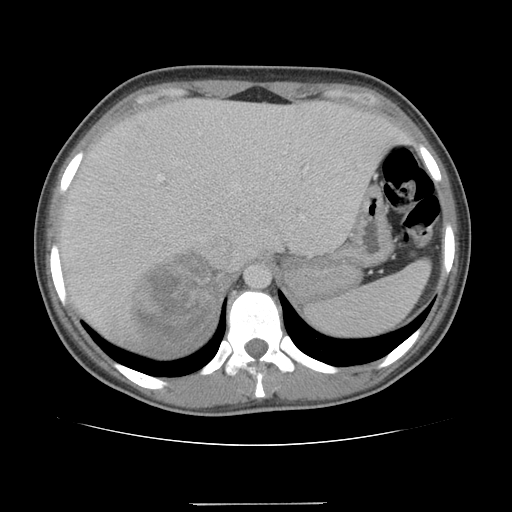
Contrast-enhanced abdominal CT, one axial slice. Position 82 of 100 along the scan axis. Reconstruction kernel STANDARD. Intravenous contrast given. Soft-tissue window (W 400 / L 40 HU). 5 mm slice thickness. 512 × 512 image matrix, field of view 360 × 360 mm. Patient: female, 21 years. Case-level facts recorded for this patient, not image findings: diagnosis: adrenocortical carcinoma; tumour side: right adrenal.
Annotated regions visible in this slice (semi-automatically segmented with operator editing):
- mass: bounding box [x1, y1, x2, y2] px = [131, 256, 220, 349]